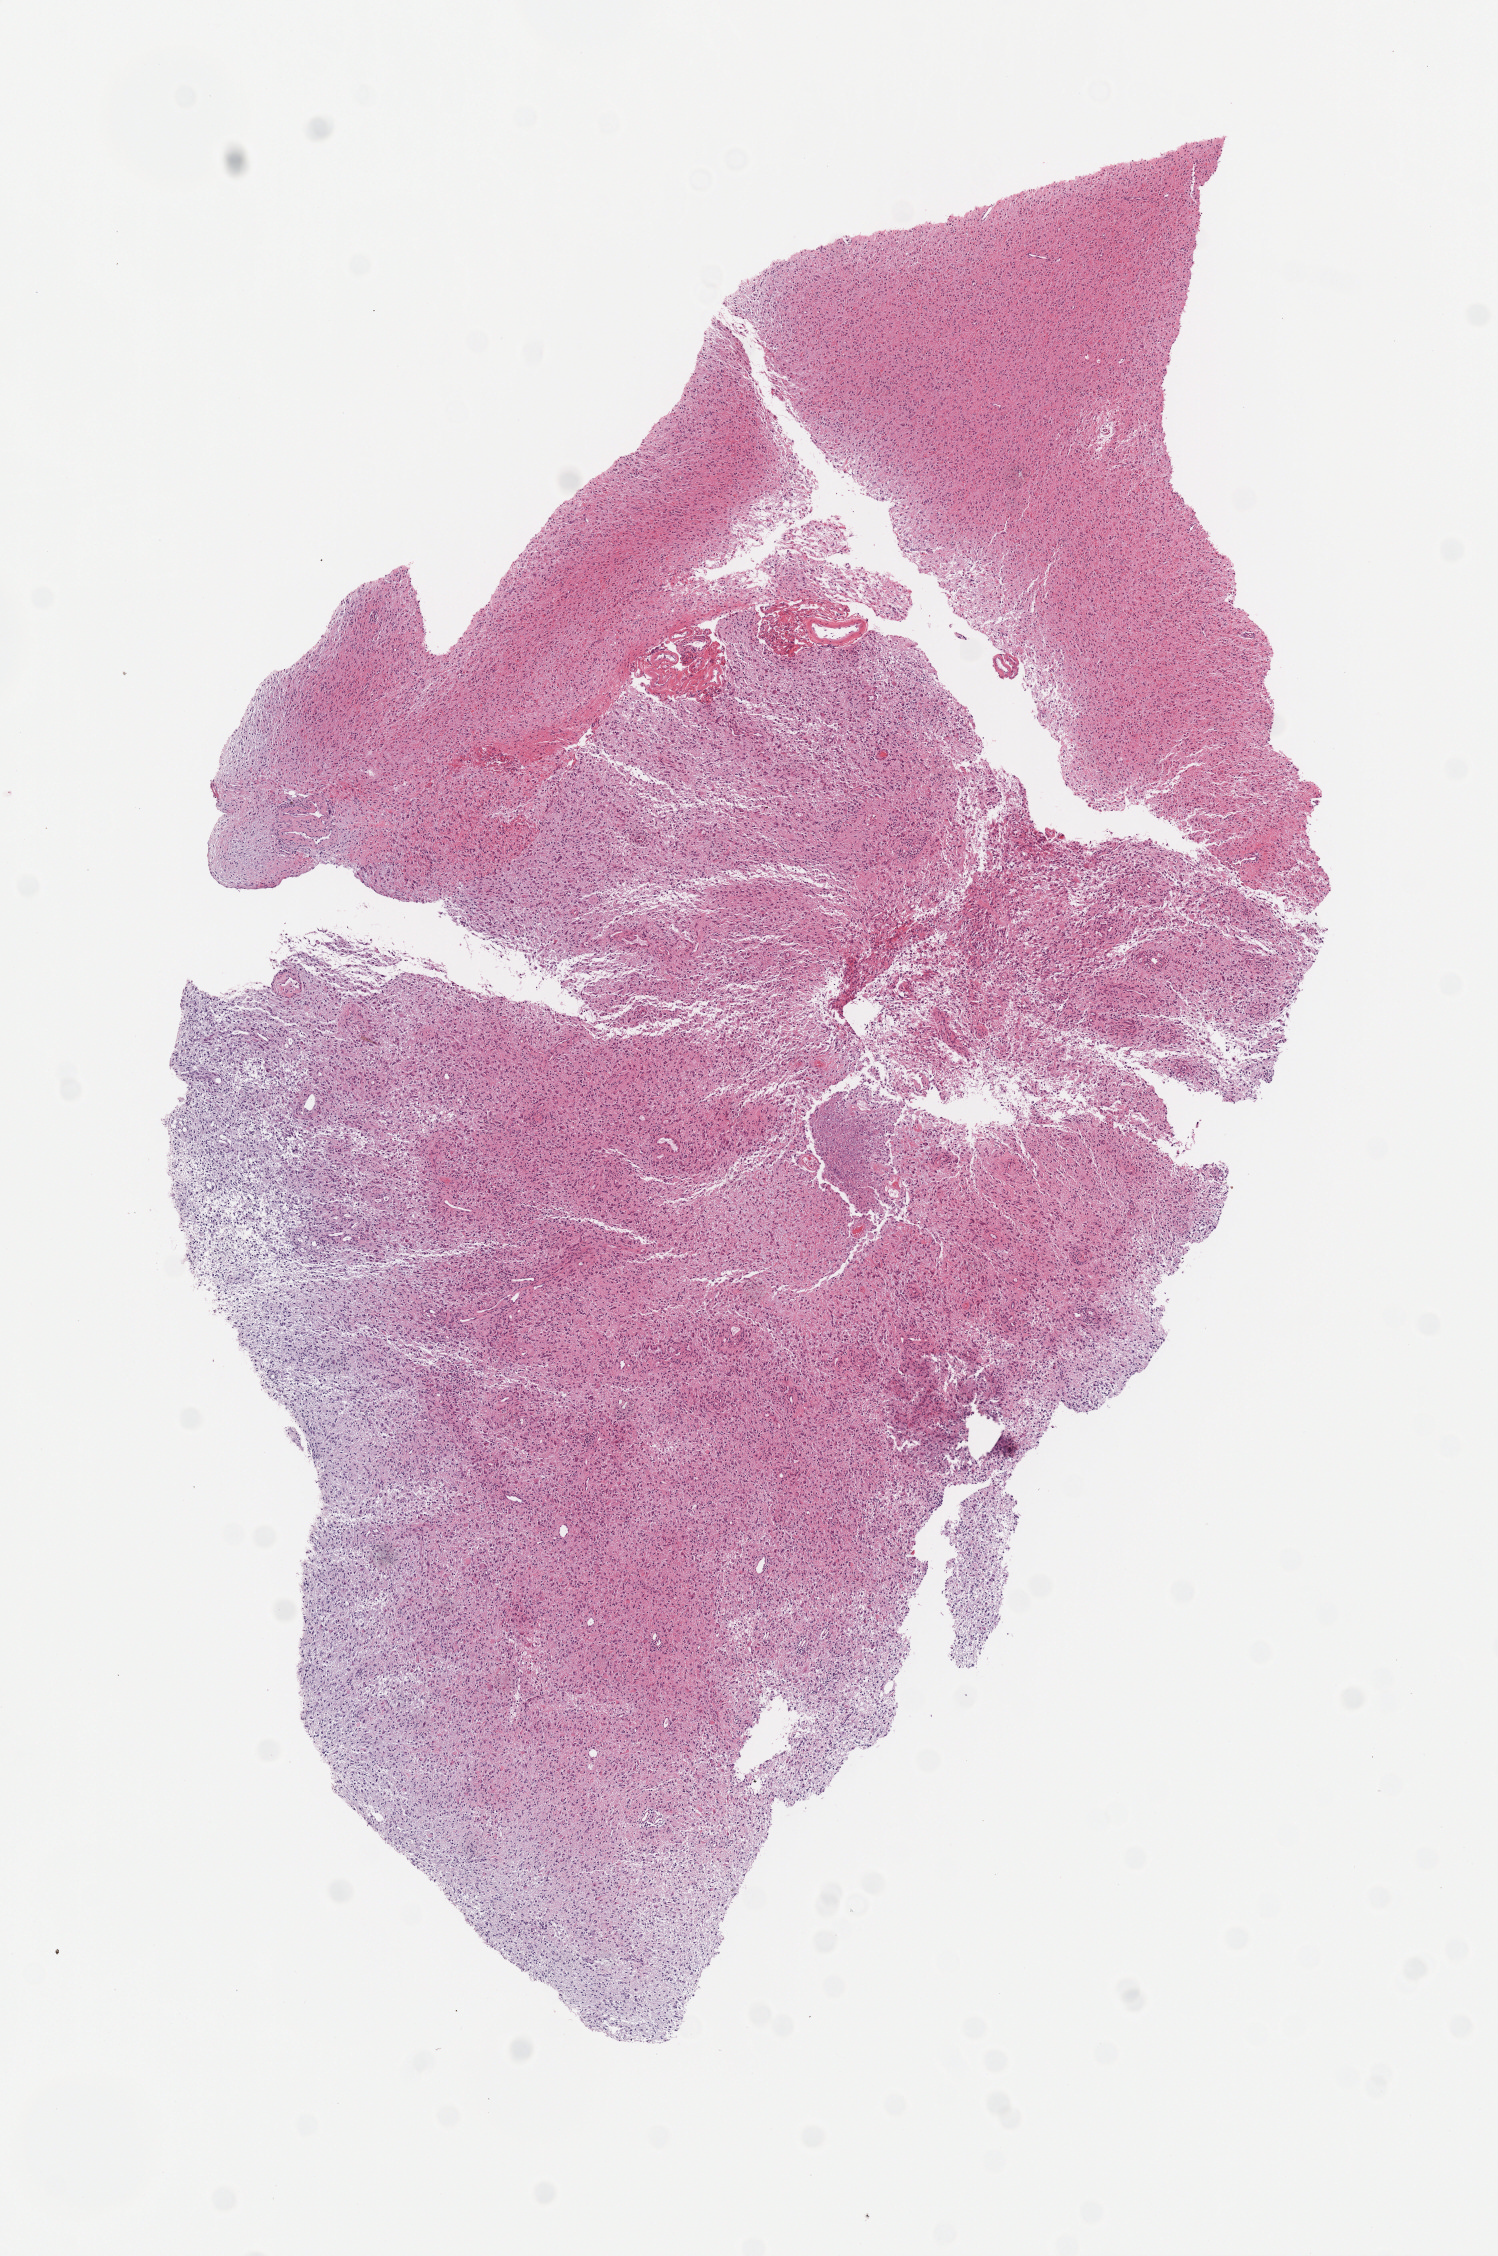
Digitized Hematoxylin and eosin (H&E) stained tissue section (whole slide), low-resolution overview of the scanned area, about 6.0 x 9.1 mm. FFPE section. Brain, primary tumour sample. Patient: female, age at initial diagnosis 57 years. Histologic grade: G3 (poorly differentiated).
Pathologic diagnosis: Astrocytoma, anaplastic (cerebrum).